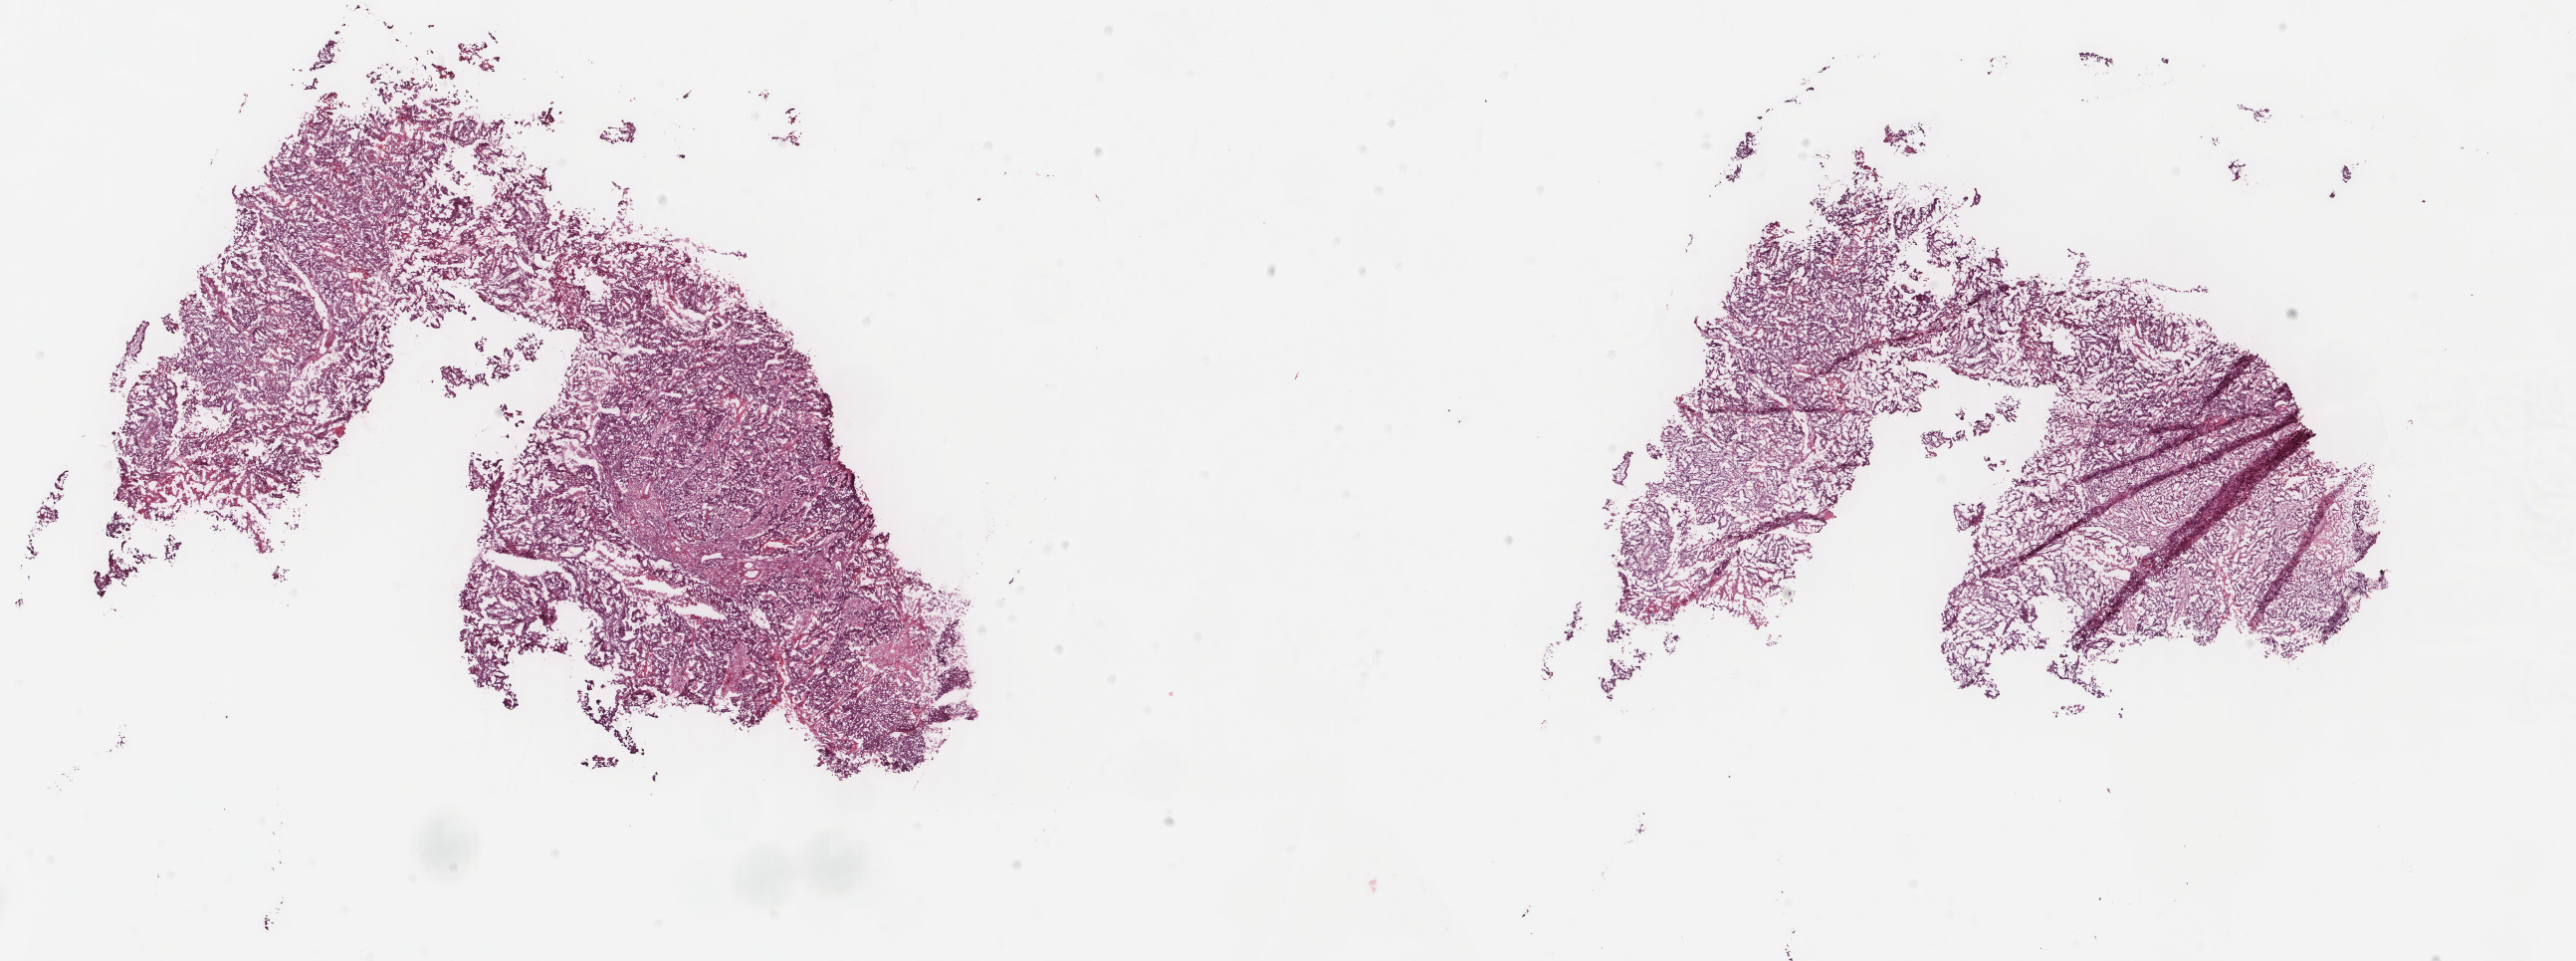
Hematoxylin and eosin (H&E) stained whole-slide image — shown as a low-resolution overview of the whole scanned area (about 20.5 x 7.7 mm, acquisition: 40x scan); frozen section; primary tumour sample from the uterus. Patient: female, age at initial diagnosis 54 years. Histologic grade: G3 (poorly differentiated). Pathologist review of this section (percent, as recorded): tumour cells 75%, tumour nuclei 90%, normal cells 13%, stromal cells 2%, necrosis 10%. Infiltration values recorded for this section: lymphocyte infiltration 1%, monocyte infiltration 0%, neutrophil infiltration 1%.
Histologic diagnosis: Endometrioid adenocarcinoma, NOS (endometrium). FIGO stage: IIB.